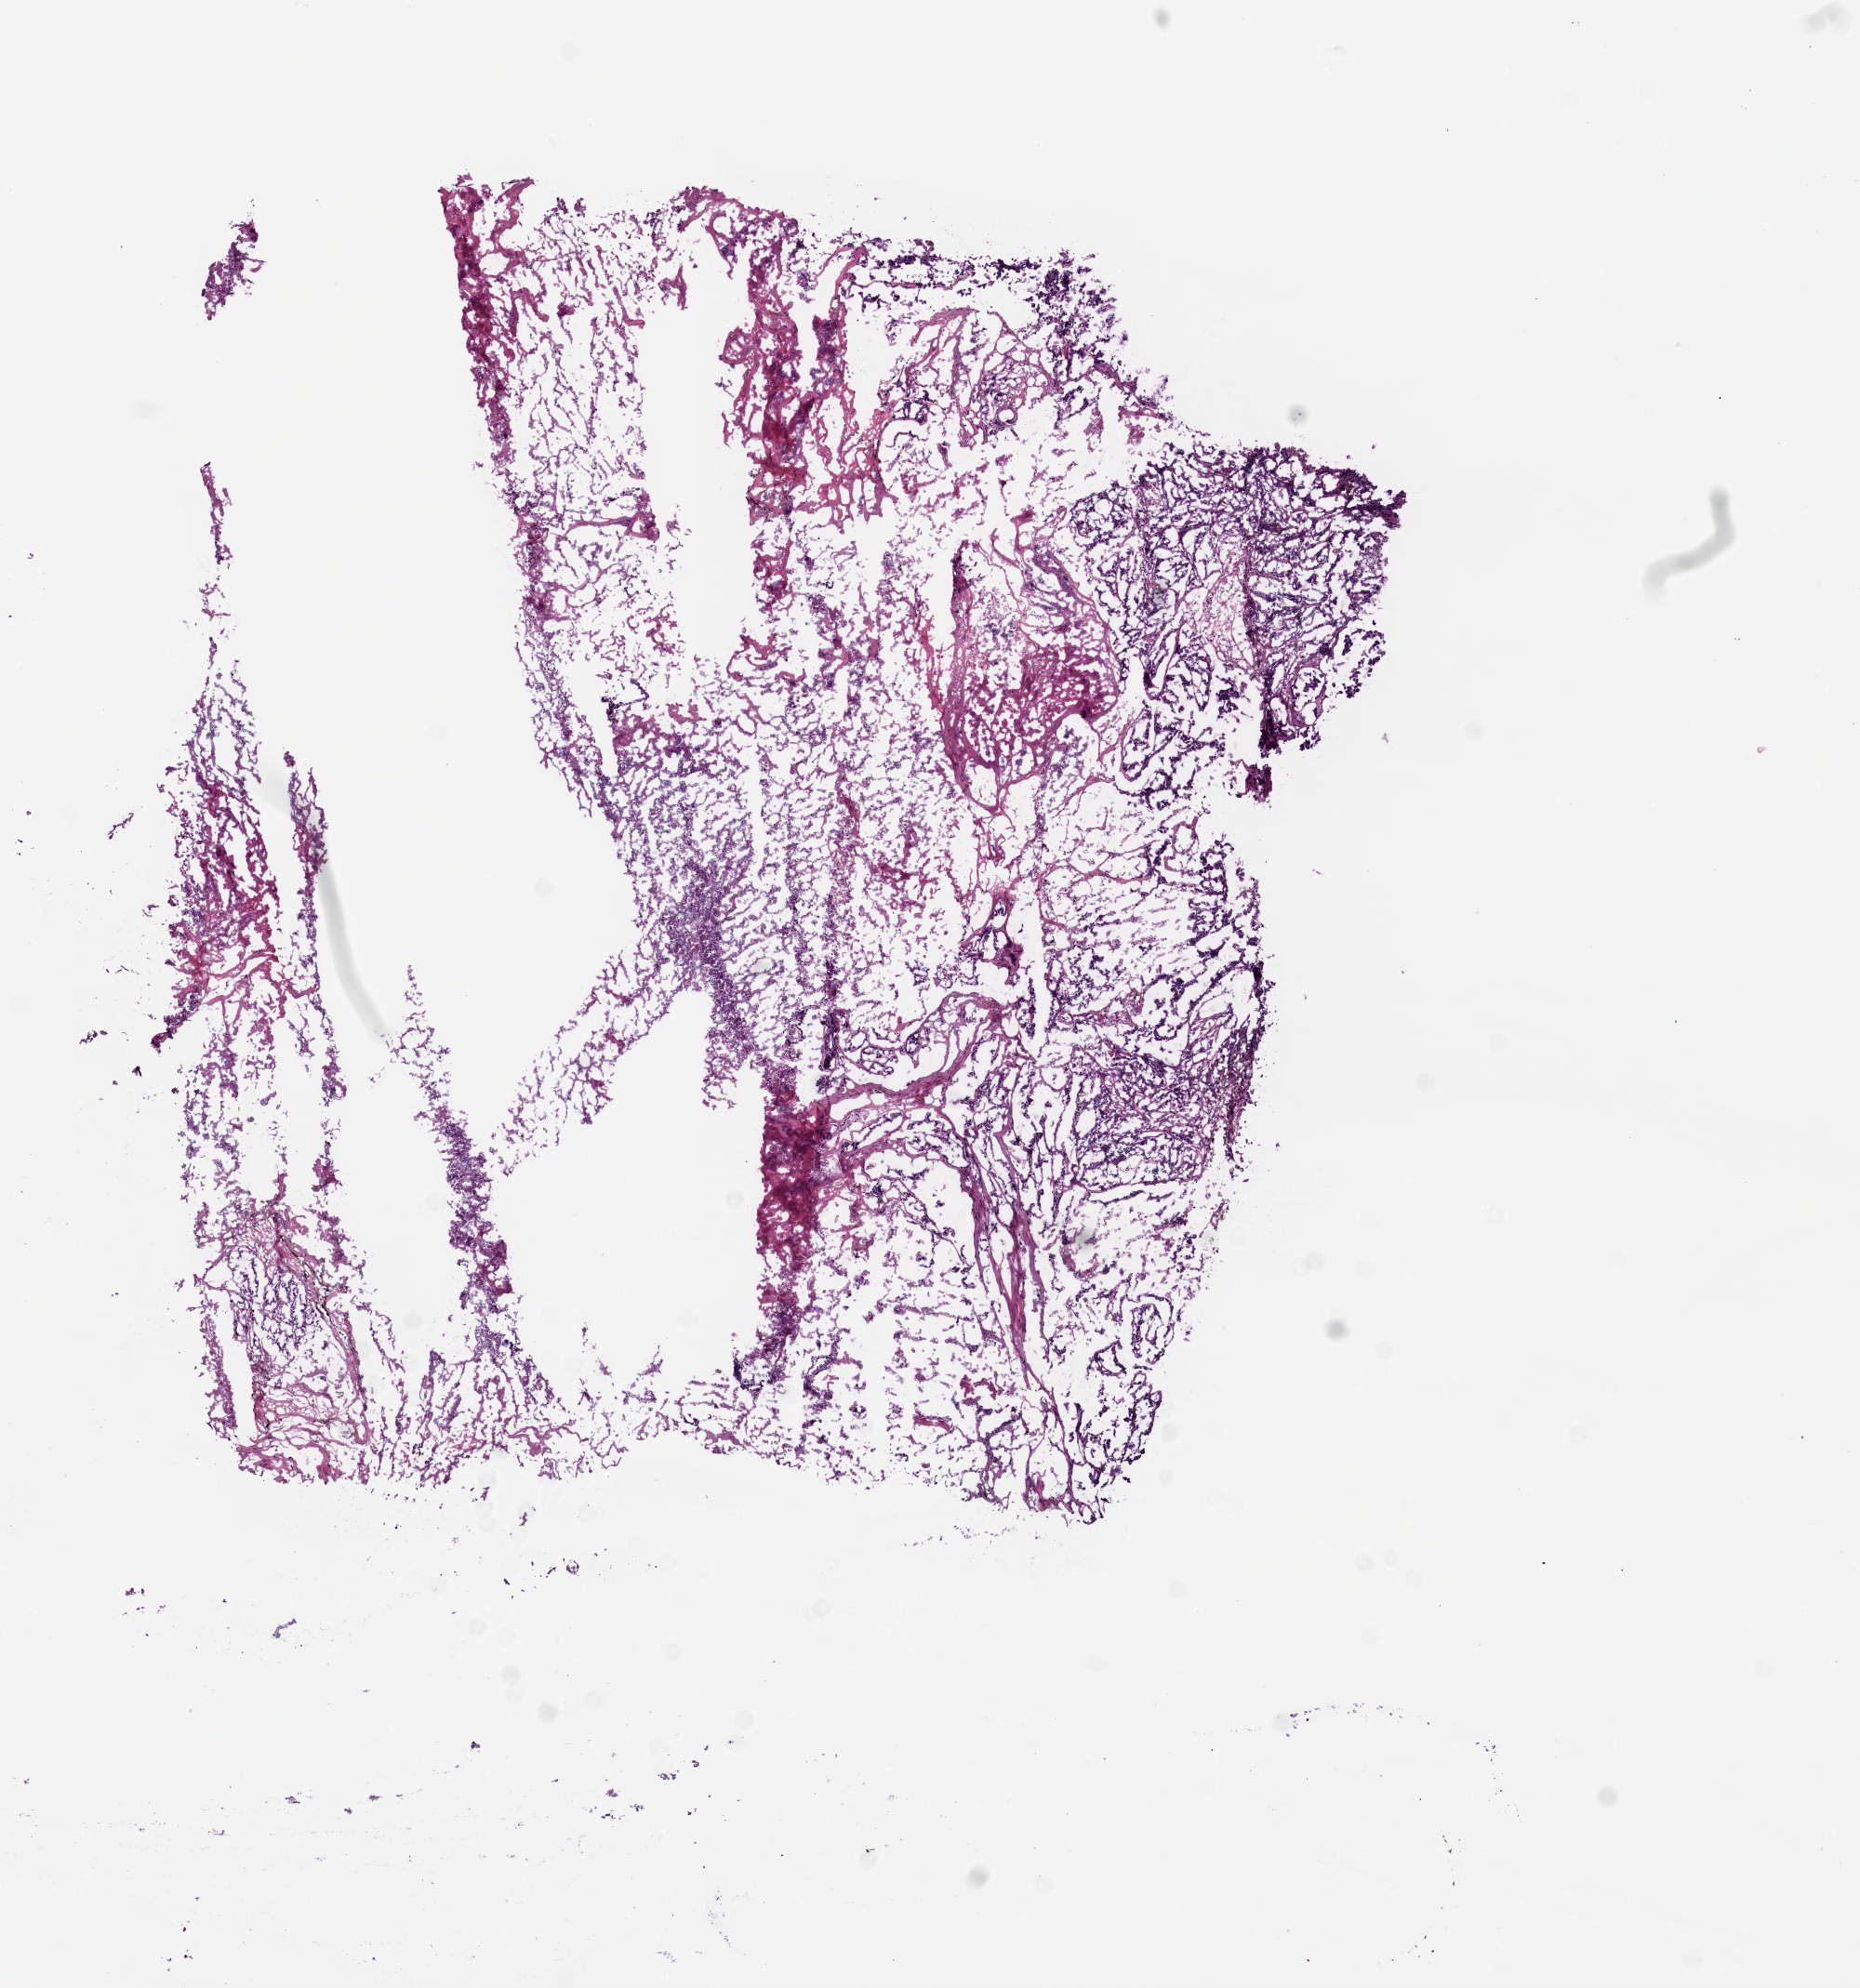
Whole-slide histology image, H&E-stained — whole scanned area (about 8.0 x 8.6 mm, from a 20x scan) shown as a low-resolution overview. Frozen section. Primary tumour sample from the lung. Patient: female, age at initial diagnosis 72 years. Composition of this section per pathologist review: tumour cells 90%, tumour nuclei 70%.
Histologic diagnosis: Adenocarcinoma, NOS (upper lobe, lung).